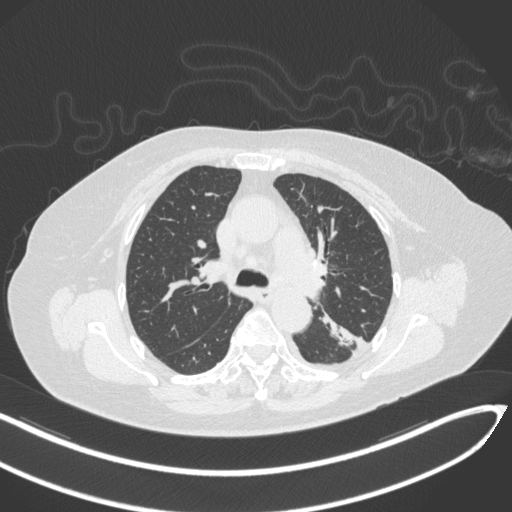
Chest CT, one axial slice. Position 208 of 270 along the scan axis. 120 kVp. Lung window (W 1500 / L -600 HU). 512 × 512 image matrix, field of view 400 × 400 mm. Female patient, age 76 years. Case-level facts recorded for this patient, not image findings: clinical TNM (as recorded): T1c N0 M0.
Outlined on this slice (bounding box drawn by a radiologist):
- lung tumour (recorded histology: adenocarcinoma): bounding box <318,311,367,357> (left, top, right, bottom; pixels)